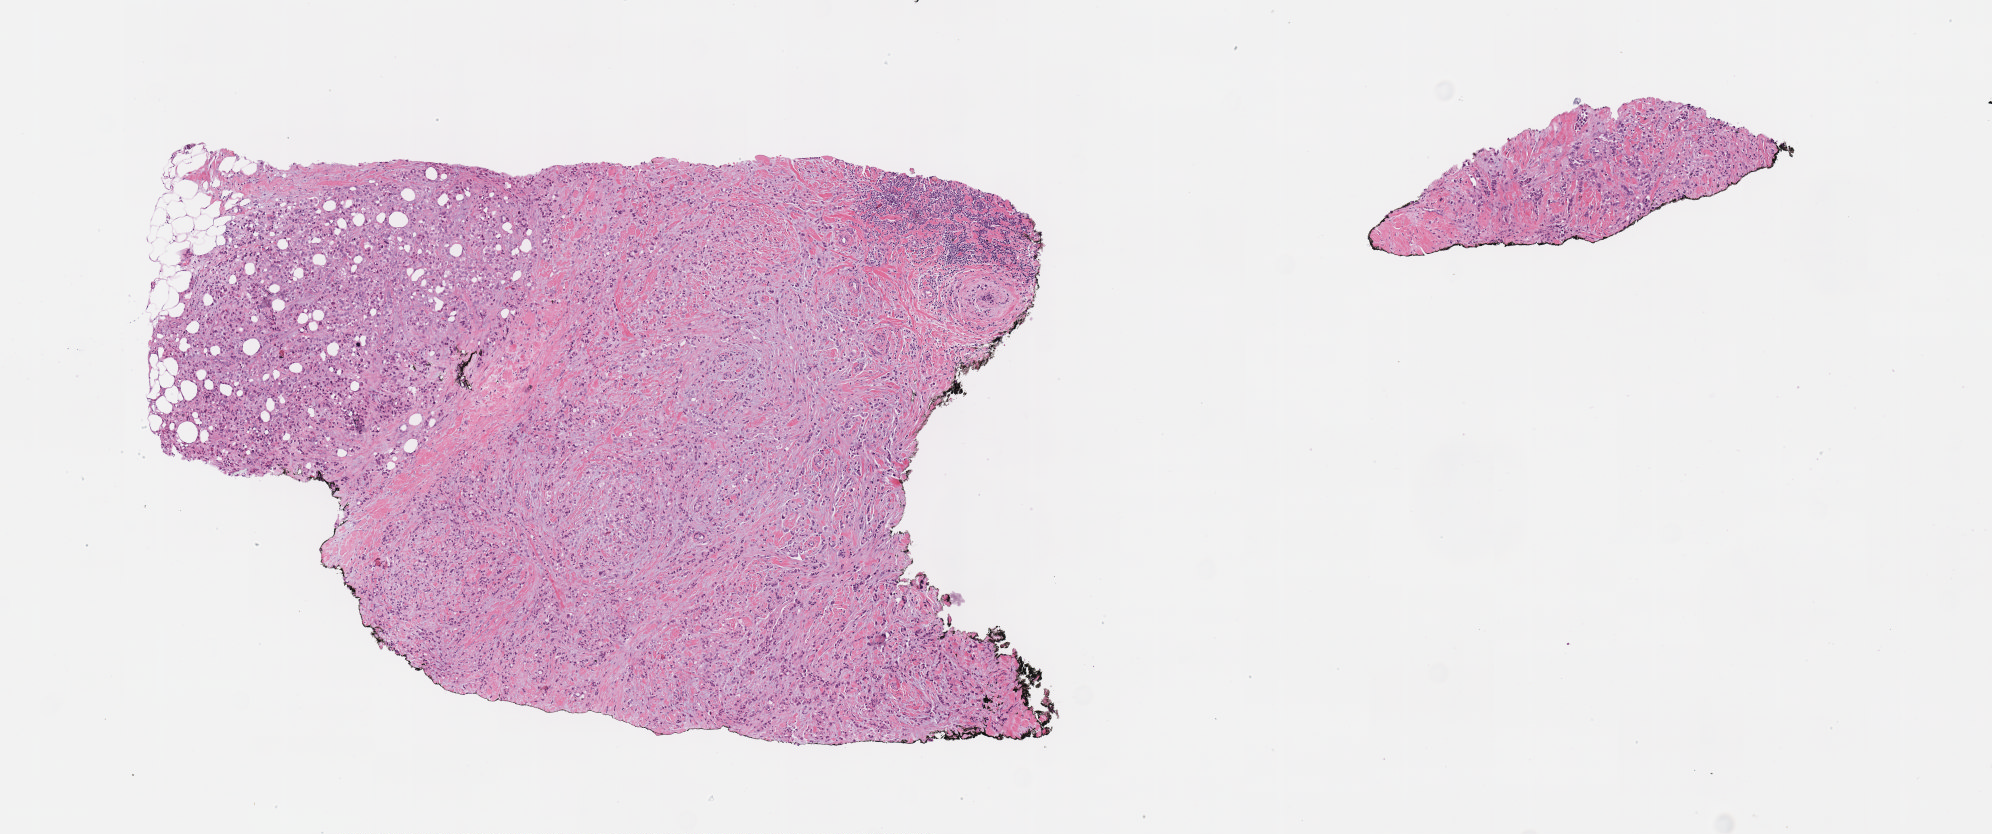
Digitized H&E tissue section (whole slide) — low-resolution overview of the scanned area, about 7.8 x 3.3 mm. FFPE section. Primary tumour sample from the breast. Patient: female, age at initial diagnosis 65 years.
Histologic diagnosis: Lobular carcinoma, NOS.